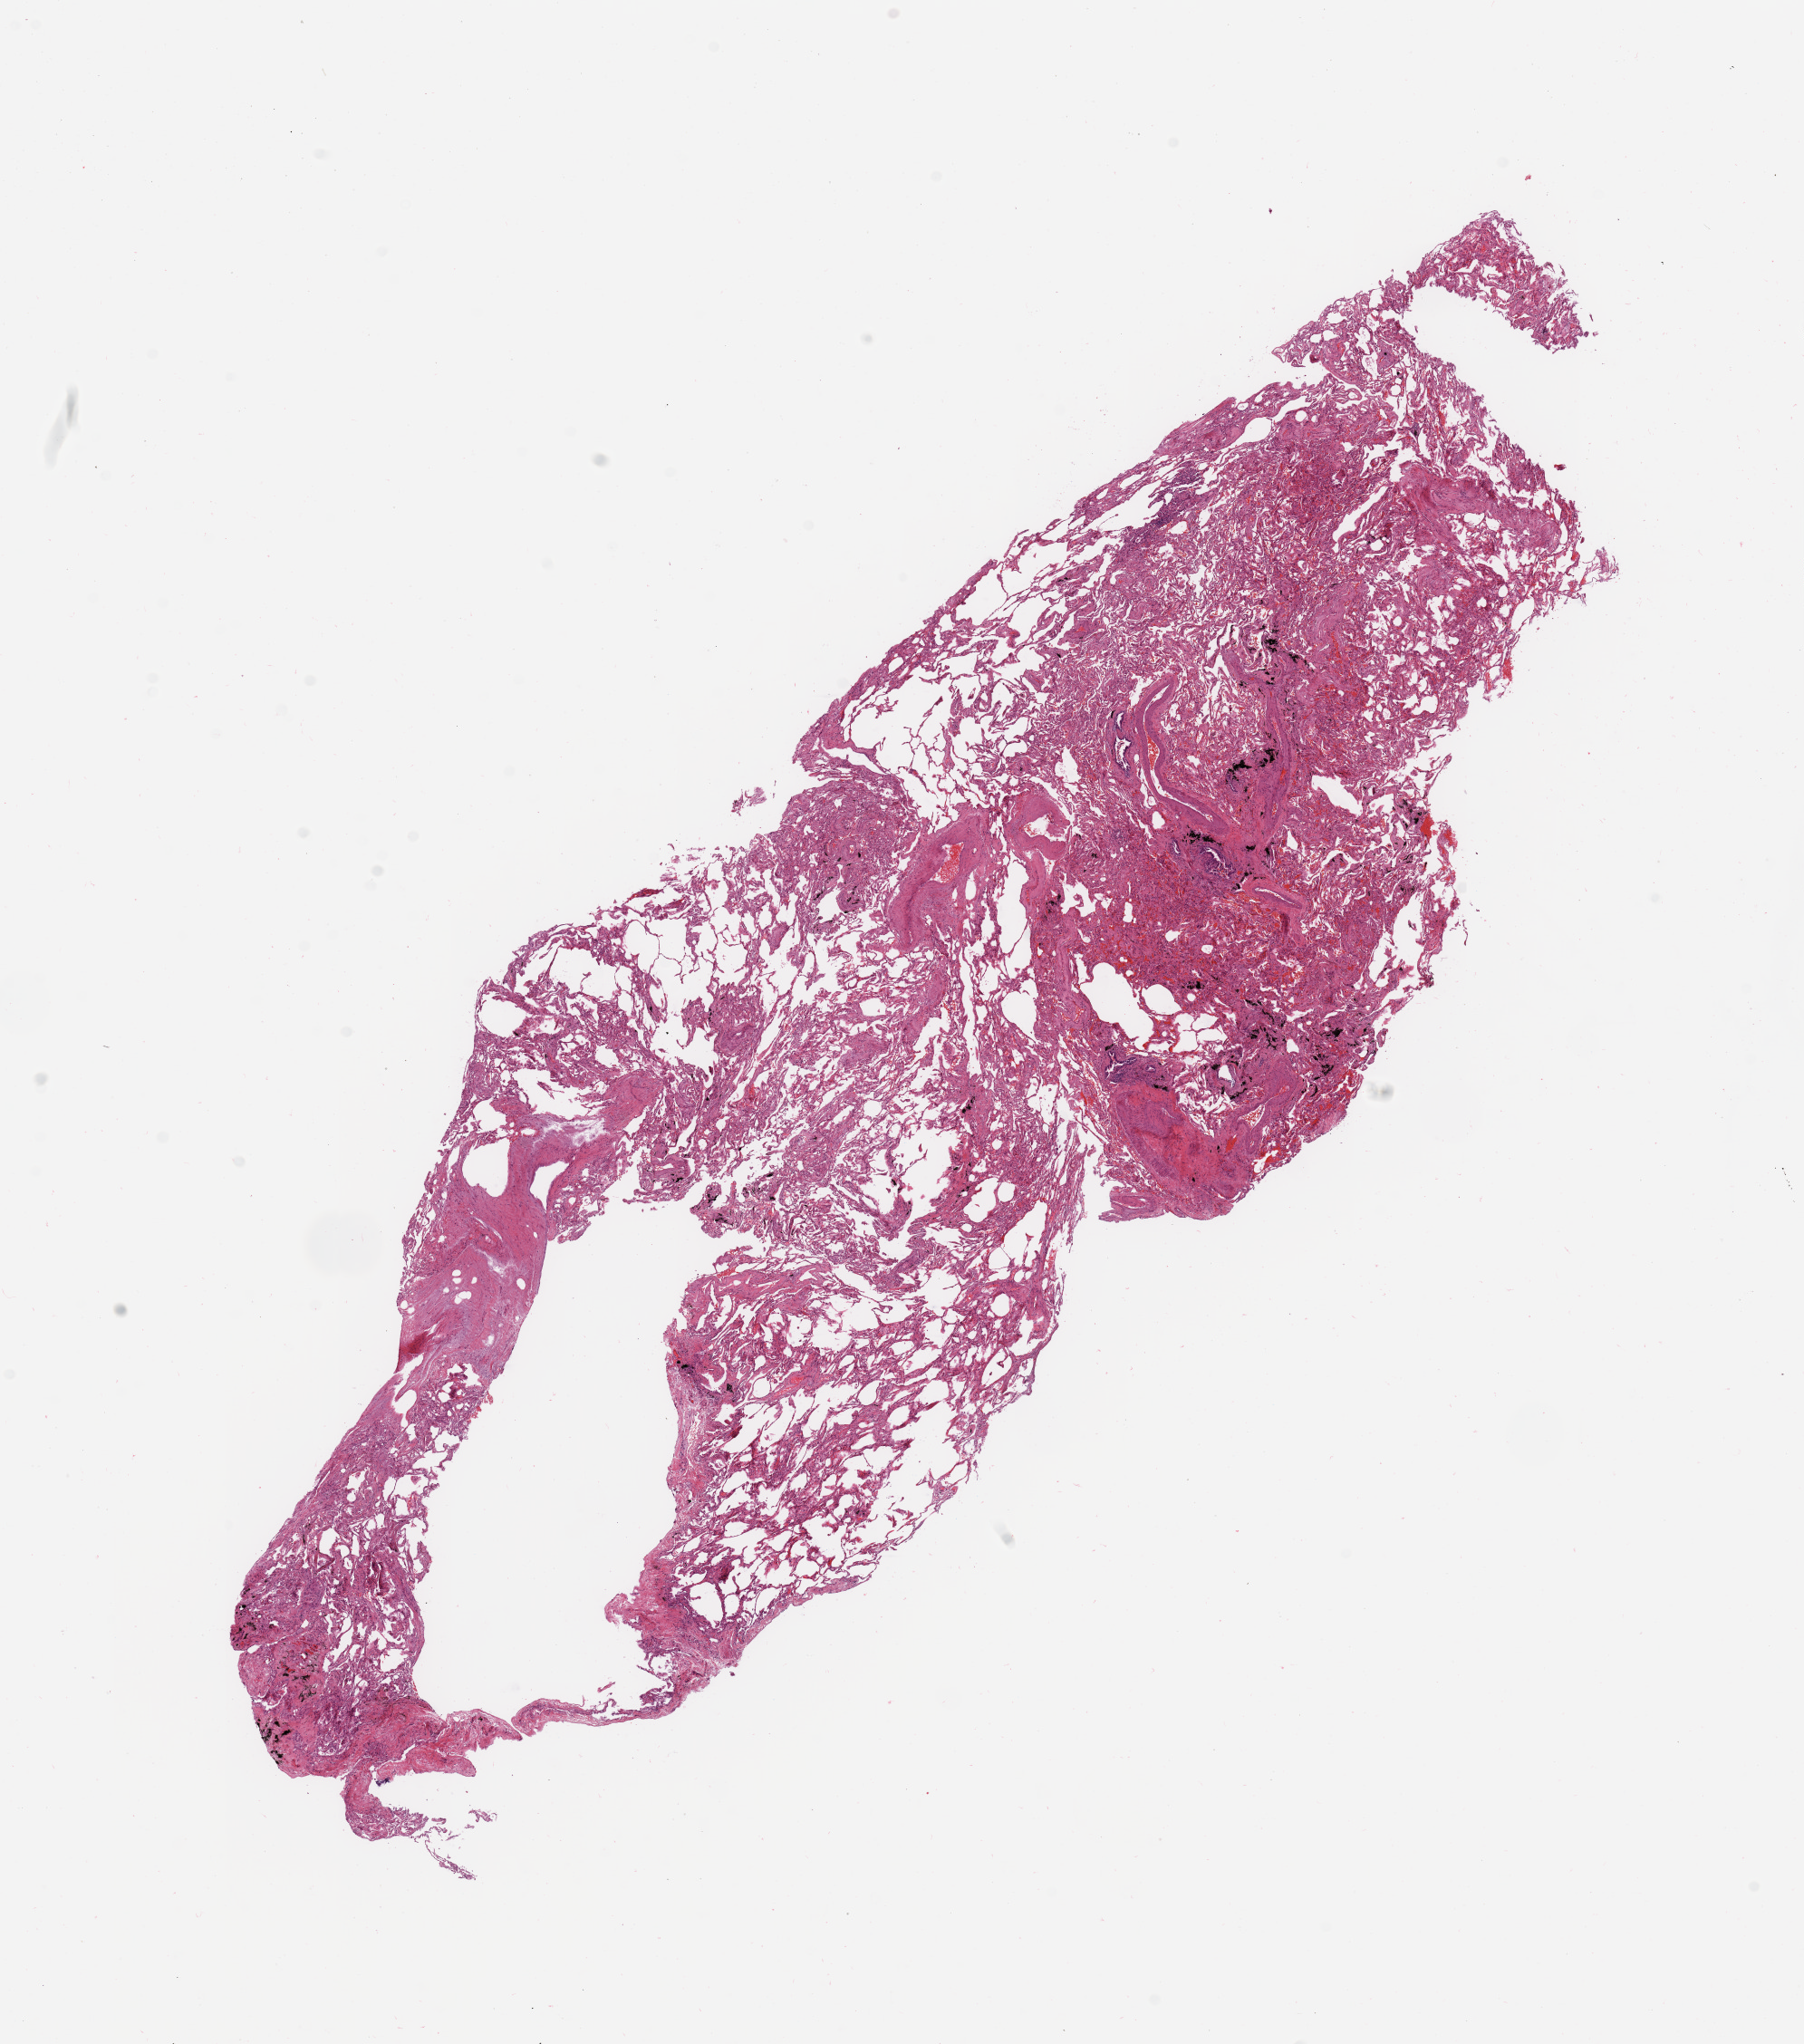
H&E whole-slide image, low-resolution overview of the scanned area, about 15.8 x 17.8 mm (from a 20x scan); normal (non-tumour) tissue sample, sampled site: lung. Patient: male, age 77 years.
- this section: normal (non-tumour) tissue from the same patient
- patient diagnosis: Adenocarcinoma, NOS